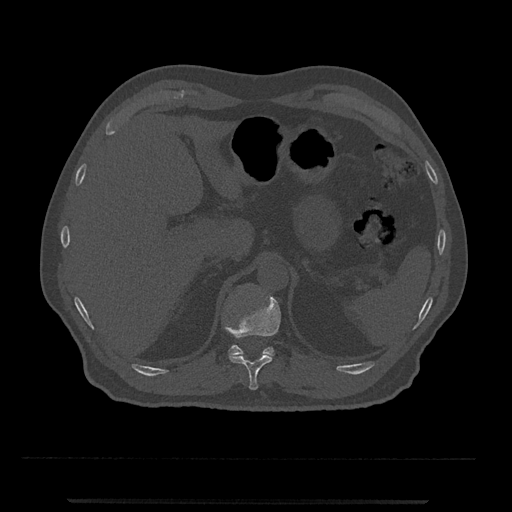
CT including the spine, one axial slice; slice 442 of 797 in the series (ordered by position); 120 kVp; bone window (W 1800 / L 400 HU); 0.5 mm slice thickness; 512 × 512 image matrix, field of view 419 × 419 mm. Patient: male, 63 years. Case-level facts recorded for this patient, not image findings: primary cancer: prostate.
Outlined on this slice (semi-automatic segmentation, software-assisted and operator-edited):
- T11 vertebra: bounding box (x1, y1, x2, y2) in pixels: (225, 293, 281, 390)
- T12 vertebra: (228, 345, 275, 356)